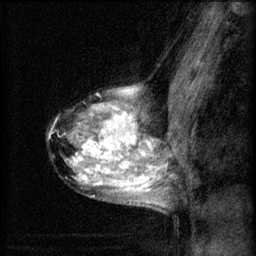
Breast MRI (dynamic contrast-enhanced), one sagittal slice. Position 43 of 60 along the scan axis. 3 images stored at this slice position (order not interpretable as contrast timing). 1.5 T. TE 4.2 ms, TR 8.2 ms. 256 × 256 image matrix. Female patient, age 40 years.
Annotated regions visible in this slice (semi-automatic segmentation, software-assisted and operator-edited):
- analysis volume of interest (the breast-tissue region the enhancement analysis was run in; not a lesion): box from (x=47, y=80) to (x=167, y=211) px
- tumour enhancement mask (voxels above the 70 % enhancement threshold inside the analysis volume of interest): (x=65, y=88)–(x=160, y=205)